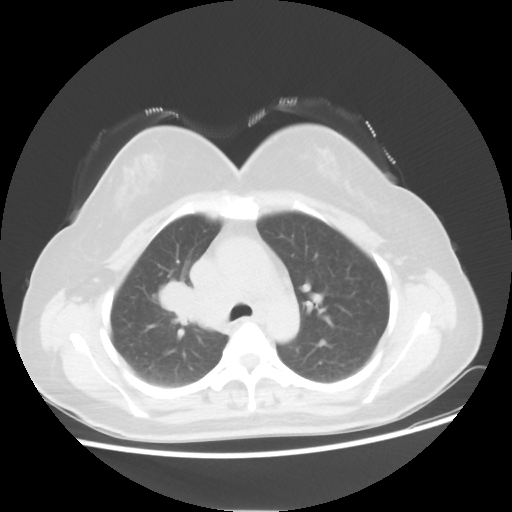
Chest CT, one axial slice; slice 35 of 50 in the series (ordered by position); lung window (W 1500 / L -600 HU); 512 × 512 image matrix, field of view 360 × 360 mm. Female patient, age 40 years. Case-level facts recorded for this patient, not image findings: clinical TNM (as recorded): T1c N3 M0; histopathological grade: G3.
Outlined on this slice (bounding box drawn by a radiologist):
- lung tumour (recorded histology: small cell carcinoma): bounding box [x1, y1, x2, y2] px = [157, 271, 195, 321]